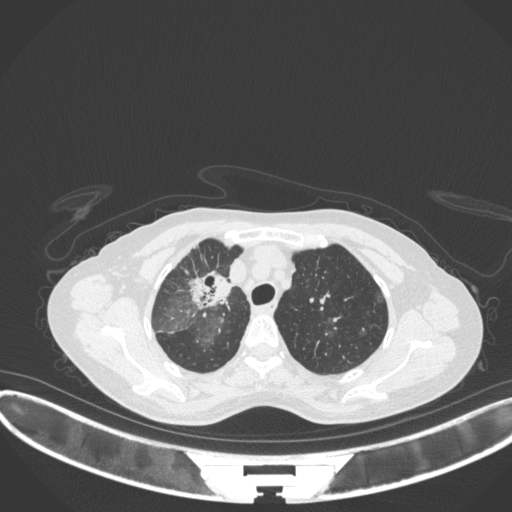
Chest CT, one axial slice. Position 253 of 311 along the scan axis. Reconstruction kernel B31f. 120 kVp. Lung window (W 1500 / L -600 HU). 1 mm slice thickness. 512 × 512 image matrix, field of view 400 × 400 mm. Female patient, age 59 years. Case-level facts recorded for this patient, not image findings: clinical TNM (as recorded): T3 N0 M0; histopathological grade: G1.
Structures marked on this image (bounding box drawn by a radiologist):
- lung tumour (recorded histology: adenocarcinoma): box from (x=190, y=267) to (x=233, y=309) px